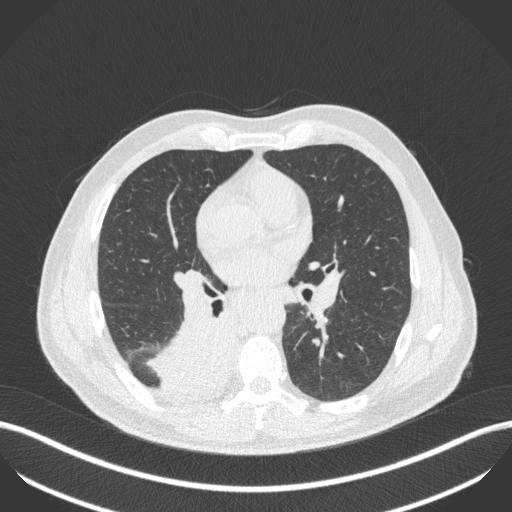
Chest CT, one axial slice. Position 250 of 451 along the scan axis. Lung window (W 1500 / L -600 HU). 1 mm slice thickness. 512 × 512 image matrix, field of view 400 × 400 mm. Patient: male, 61 years. Case-level facts recorded for this patient, not image findings: clinical TNM (as recorded): T1 N0 M0.
Outlined on this slice (bounding box drawn by a radiologist):
- lung tumour (recorded histology: small cell carcinoma): bounding box (x1, y1, x2, y2) in pixels: (143, 310, 236, 404)